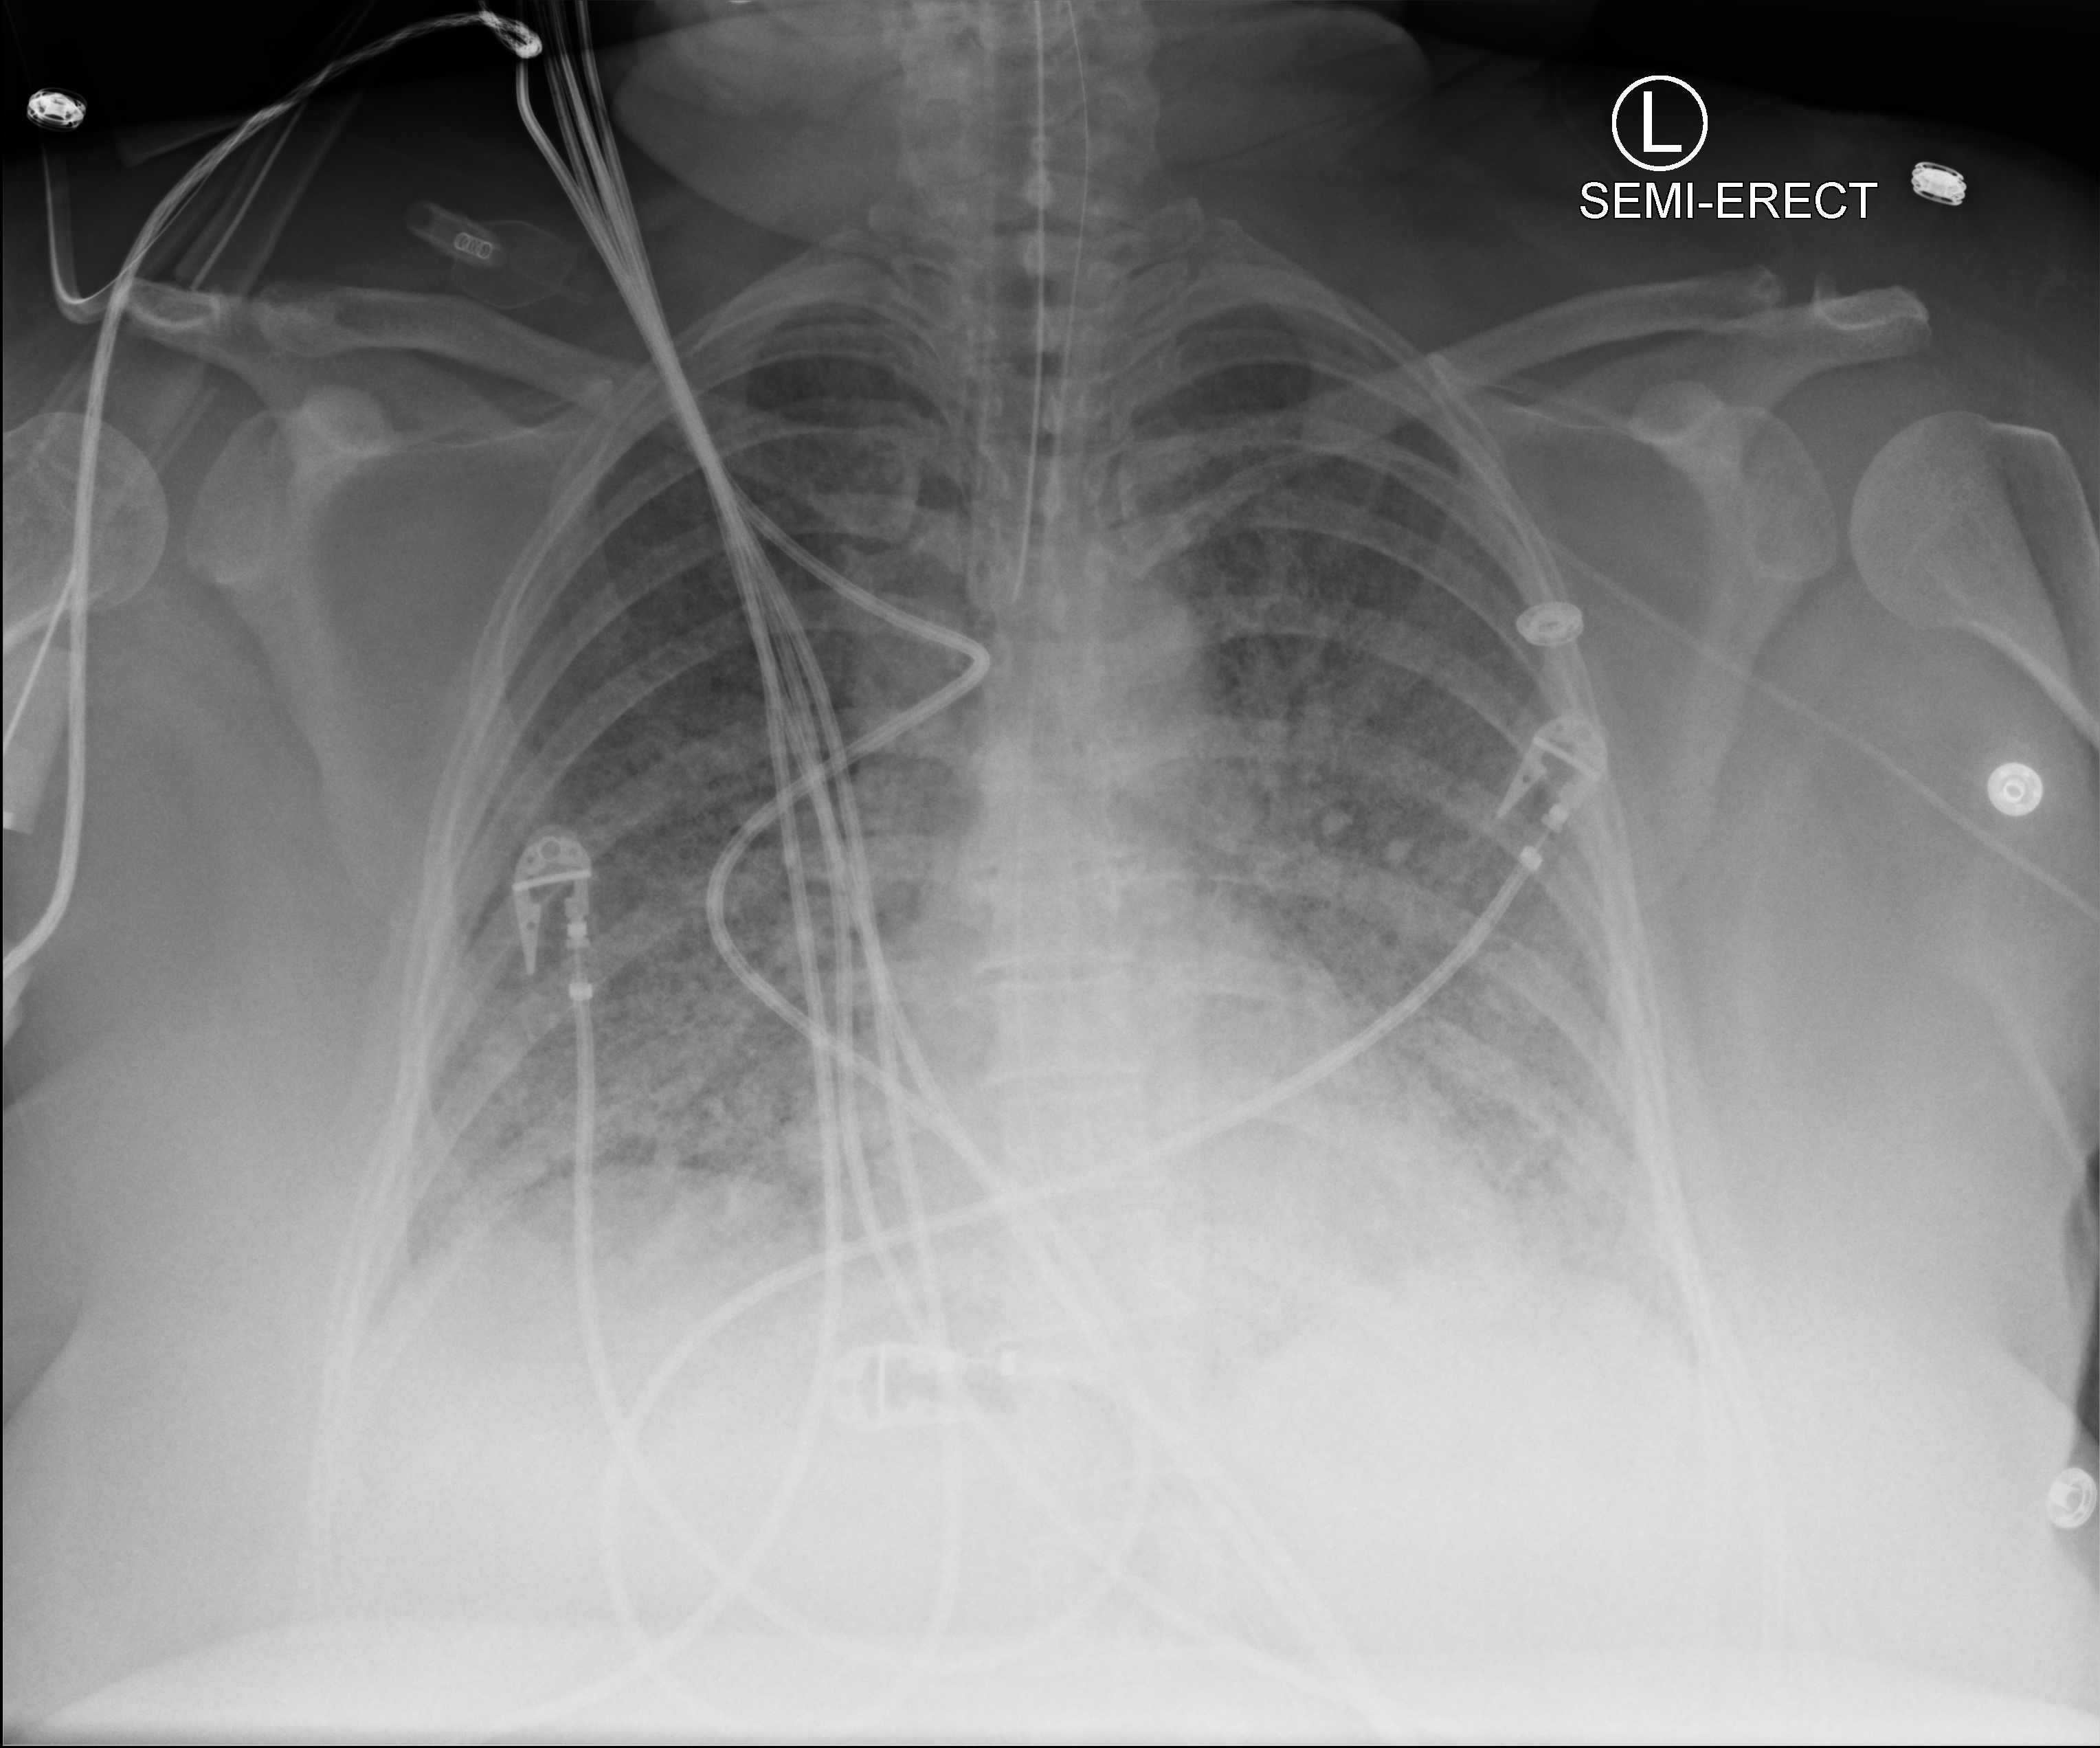
Portable chest radiograph. Patient hospitalised with COVID-19; female, aged 18–59 years.
Admission-level facts for this patient (not findings on this image; timing relative to this image not recorded): diabetes (admission record): no.